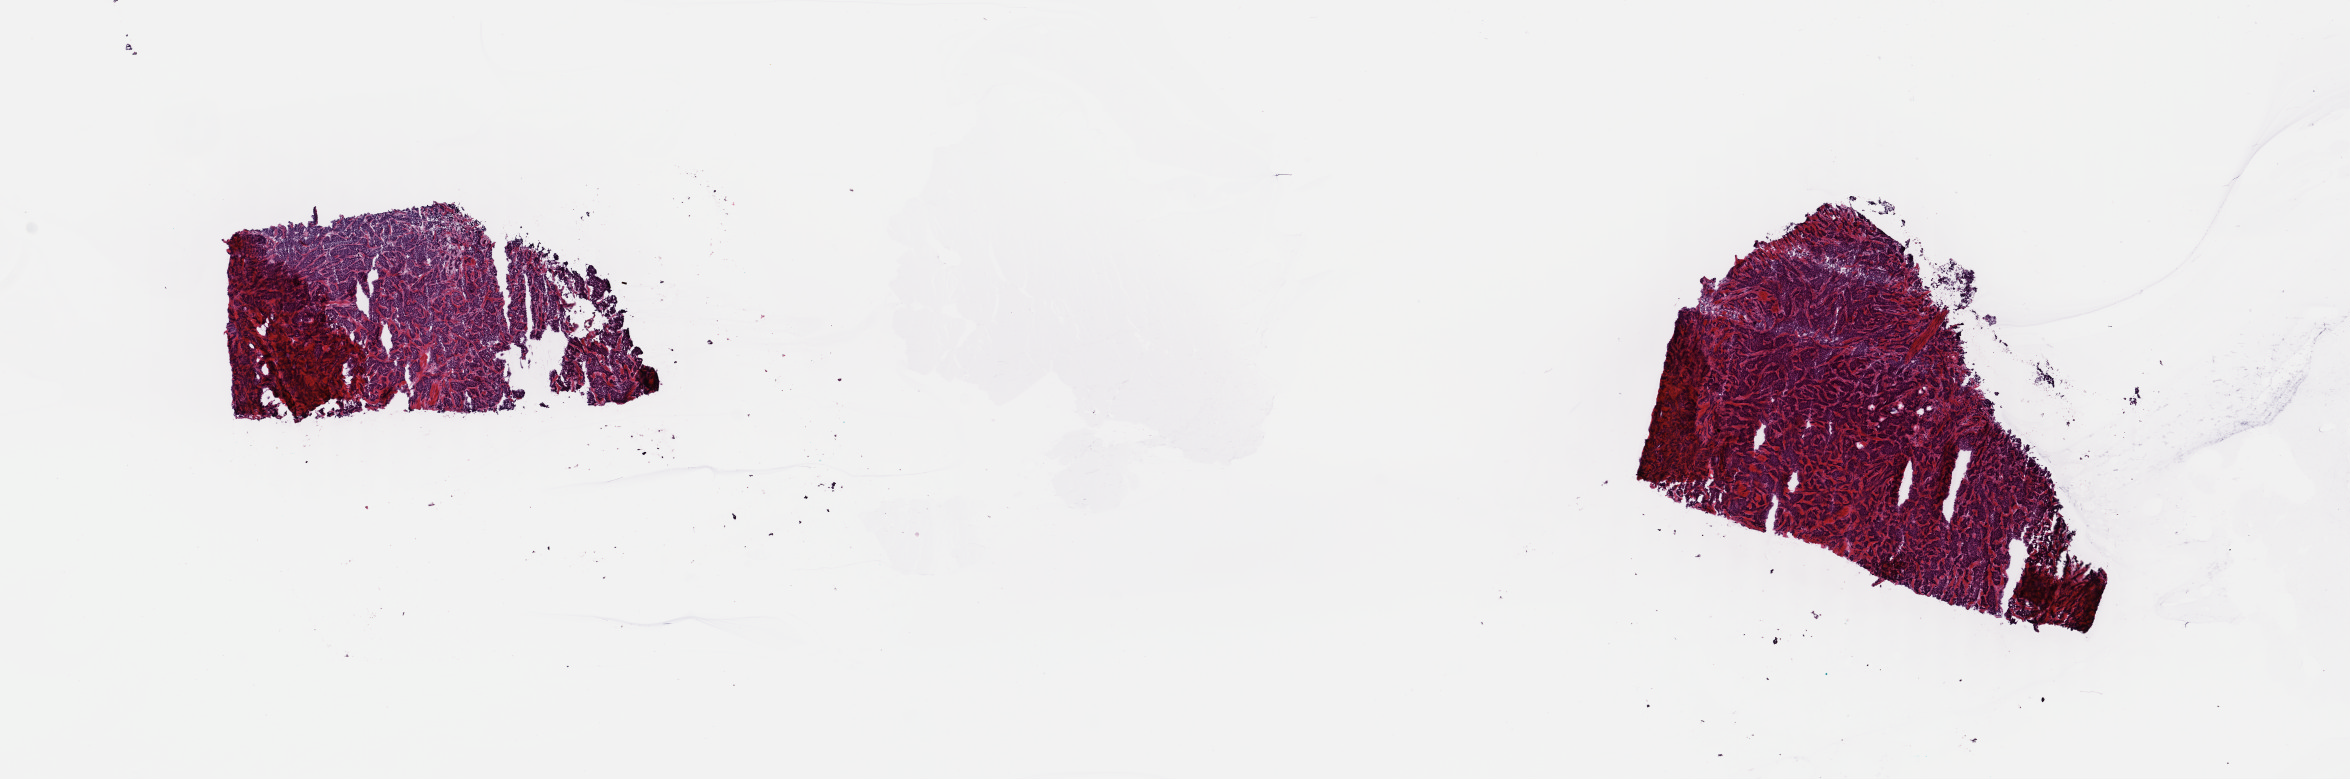
Digitized H&E-stained tissue section (whole slide) — a low-resolution overview of the entire scanned area, about 18.5 x 6.1 mm. Frozen section from the top of the tissue portion. Primary tumour sample from the breast. Female patient; age at initial diagnosis 64 years.
Diagnosis: Infiltrating duct carcinoma, NOS.